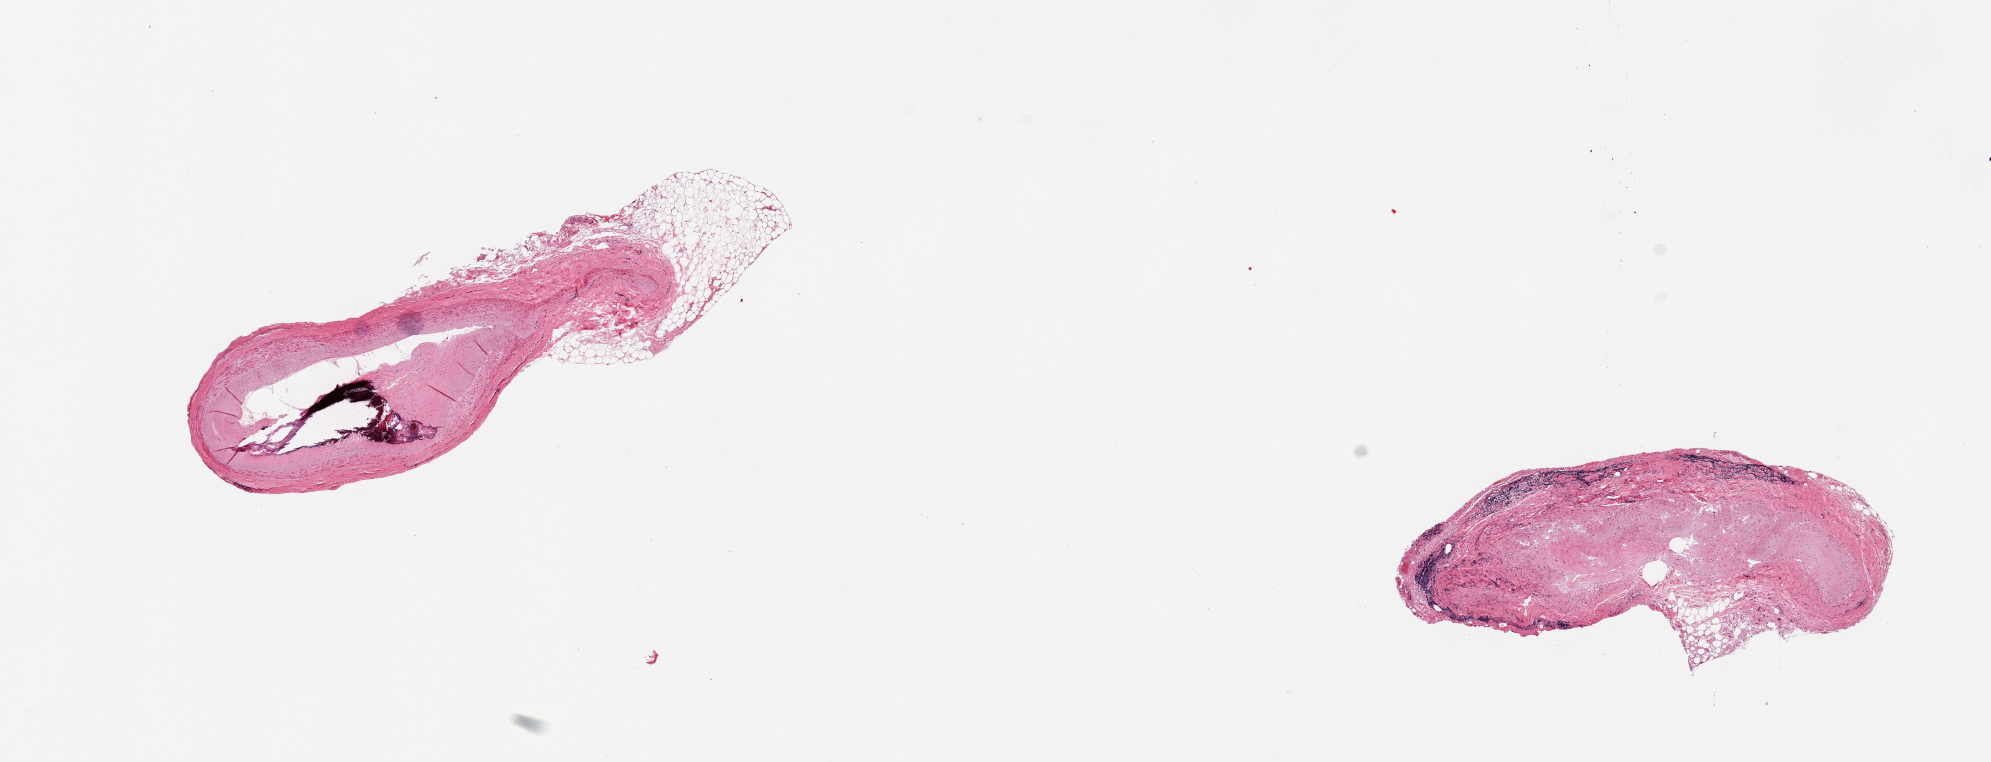
Whole-slide image, hematoxylin and eosin (H&E) stain, shown as a low-resolution overview of the whole scanned area (about 15.8 x 6.0 mm), PAXgene-fixed paraffin-embedded (PFPE) section, target tissue: coronary artery, donor tissue sample. Donor sex: female.
Pathologist's review note for this sample: 2 pieces; calcific atherosclerosis with narrowing of the lumen (50-75%), attachment of fat up to 20%, peripheral cuff of lymphocytes in 1 piece.